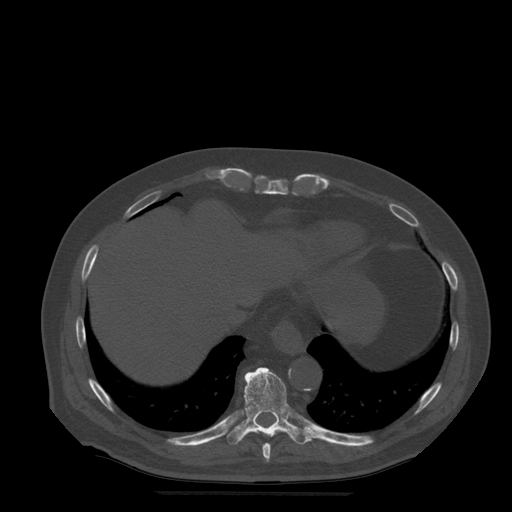
CT including the spine, one axial slice. Slice 273 of 522 in the series (ordered by position). Bone window (W 1800 / L 400 HU). 512 × 512 image matrix, field of view 420 × 420 mm. Patient age 72 years. Case-level facts recorded for this patient, not image findings: primary cancer: prostate.
Annotated regions visible in this slice (semi-automatic segmentation, software-assisted and operator-edited):
- T10 vertebra: bounding box (x1, y1, x2, y2) in pixels: (227, 368, 313, 445)
- T9 vertebra: (262, 443, 271, 462)